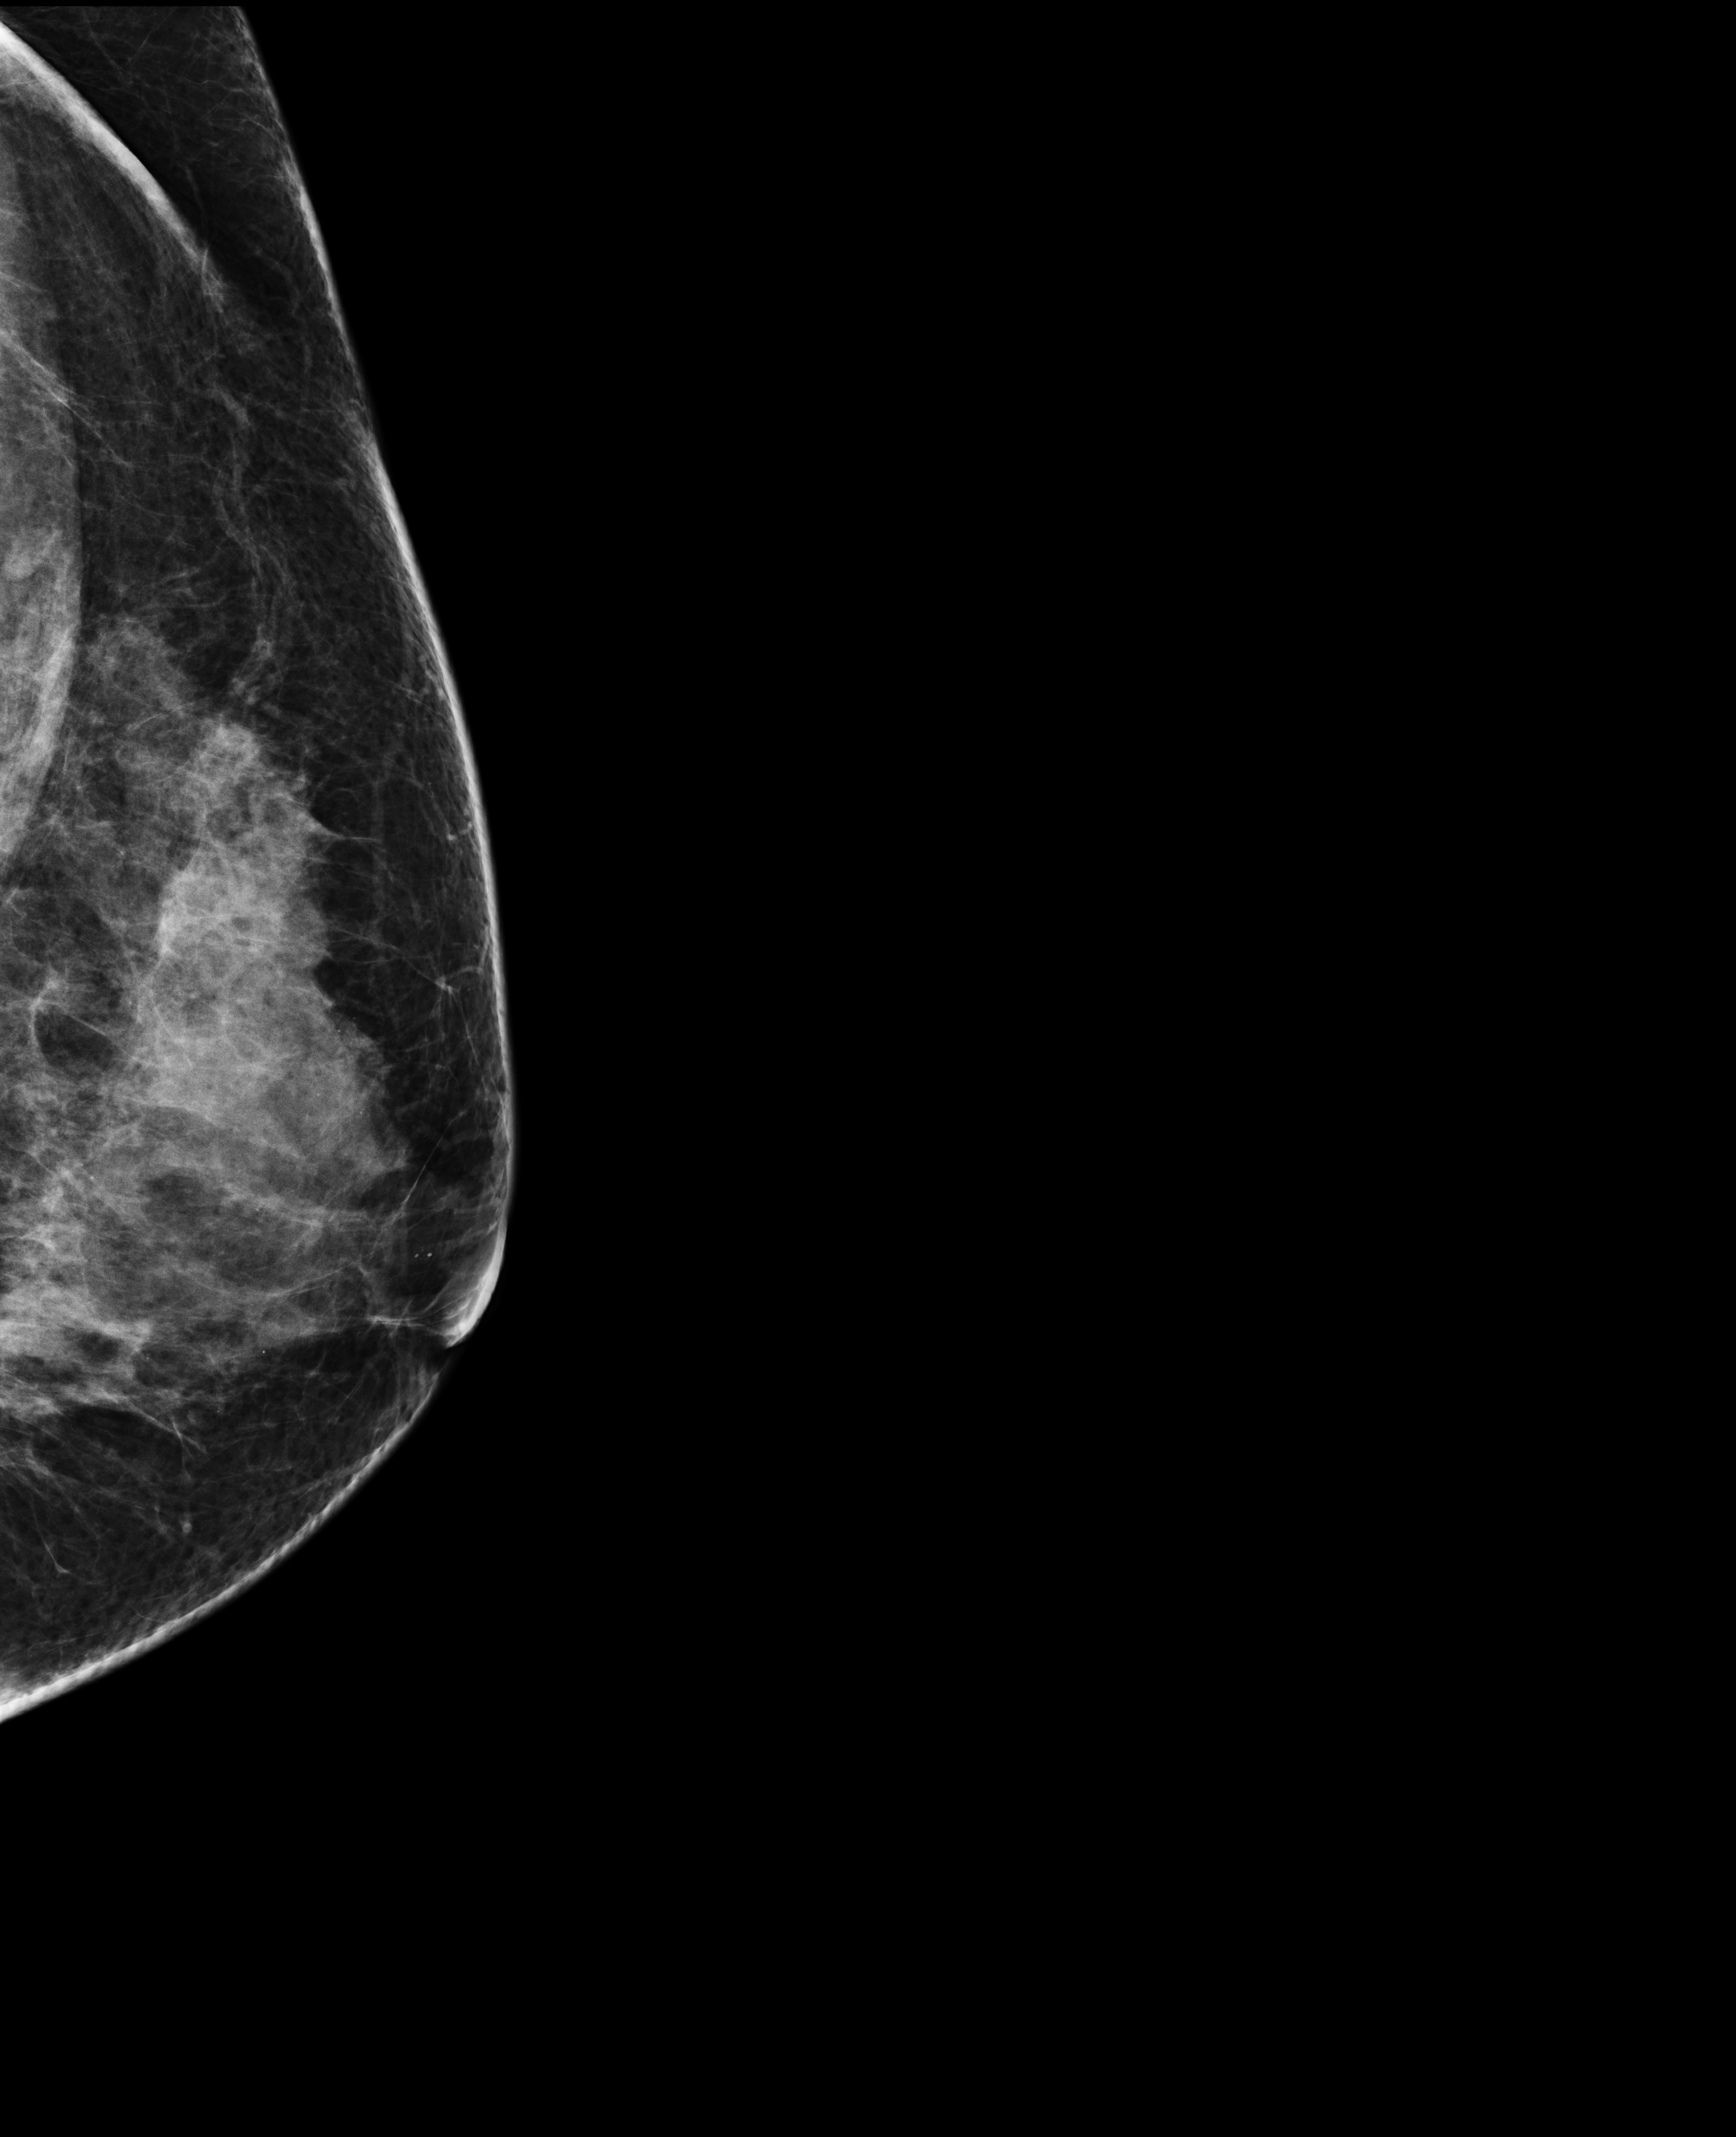
Digital mammogram (FFDM); left breast; laterally exaggerated craniocaudal (XCCL) view; annual screening mammography examination; system: Selenia Dimensions. Patient aged 48 years (female).
Breast density at the screening exam (both breasts): heterogeneously dense (BI-RADS density category c). Final BI-RADS assessment for this screening round (tomosynthesis exam, both breasts): category 4. Recall: recalled for additional imaging after this screen.